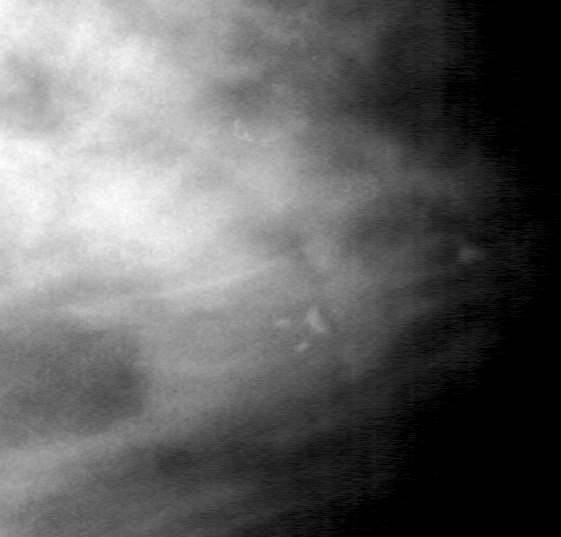
Region of interest cut from a scanned film mammogram (one marked finding), right breast, MLO view.
Marked abnormality: calcifications, morphology amorphous, distribution clustered; BI-RADS assessment category 4; subtlety rating 3 on a 1 (subtle) to 5 (obvious) scale; pathology (as recorded): benign.